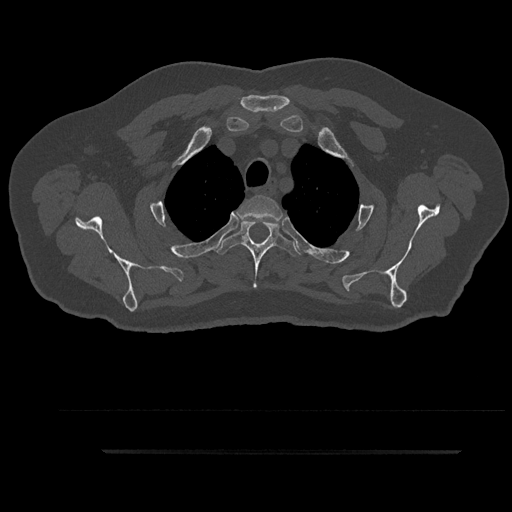
CT including the spine, one axial slice. 120 kVp. Bone window (W 1800 / L 400 HU). 0.5 mm slice thickness. 512 × 512 image matrix, field of view 432 × 432 mm. Male patient, age 63 years. Case-level facts recorded for this patient, not image findings: primary cancer: renal; vertebrae with lytic lesions (as recorded): T8.
Structures marked on this image (semi-automatically segmented with operator editing):
- T2 vertebra: bounding box [x1, y1, x2, y2] px = [237, 195, 283, 221]
- T3 vertebra: [215, 219, 301, 289]